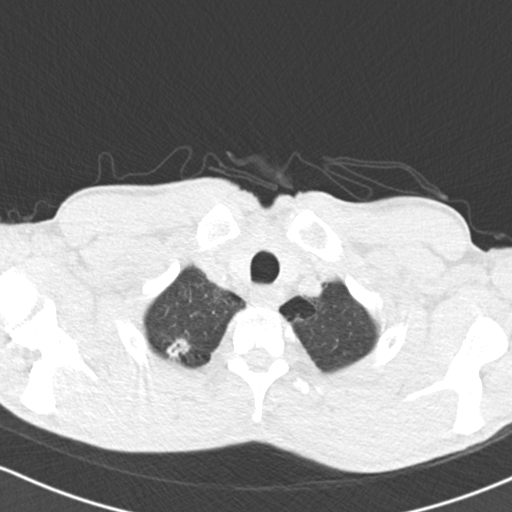
Low-dose screening chest CT, axial slice. Baseline annual screen. Lung window (W 1500 / L -600 HU). 120 kVp. Male participant, aged 64 years at enrolment. Current smoker at enrolment.
• Expert reader's lesion annotation, bounding box (x1, y1, x2, y2) in pixels: (149, 323, 202, 374).
• The exam's reader record, not a measurement of the box and not confirmed to be the same lesion: non-calcified nodule or mass ≥4 mm, right upper lobe, 13 × 11 mm, spiculated (stellate) margins, soft tissue attenuation.
• Lung cancer was diagnosed 161 days after this screen: adenocarcinoma, NOS, right upper lobe, poorly differentiated (G3), stage IA (AJCC 6th edition), 13 mm at pathology.